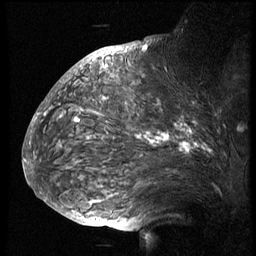
Breast MRI (dynamic contrast-enhanced), one sagittal slice; slice 44 of 74 in the series (ordered by position); 3 images stored at this slice position (order not interpretable as contrast timing); 1.5 T; TE 4.2 ms, TR 8.9 ms; 256 × 256 image matrix. Female patient, age 57 years. Case-level facts recorded for this patient, not image findings: setting: breast cancer imaged before/during neoadjuvant chemotherapy; receptor status: HER2-positive.
Outlined on this slice (semi-automatic segmentation, software-assisted and operator-edited):
- analysis volume of interest (the breast-tissue region the enhancement analysis was run in; not a lesion): bounding box (x1, y1, x2, y2) in pixels: (51, 67, 247, 173)
- tumour enhancement mask (voxels above the 140 % enhancement threshold inside the analysis volume of interest): (75, 99, 205, 153)